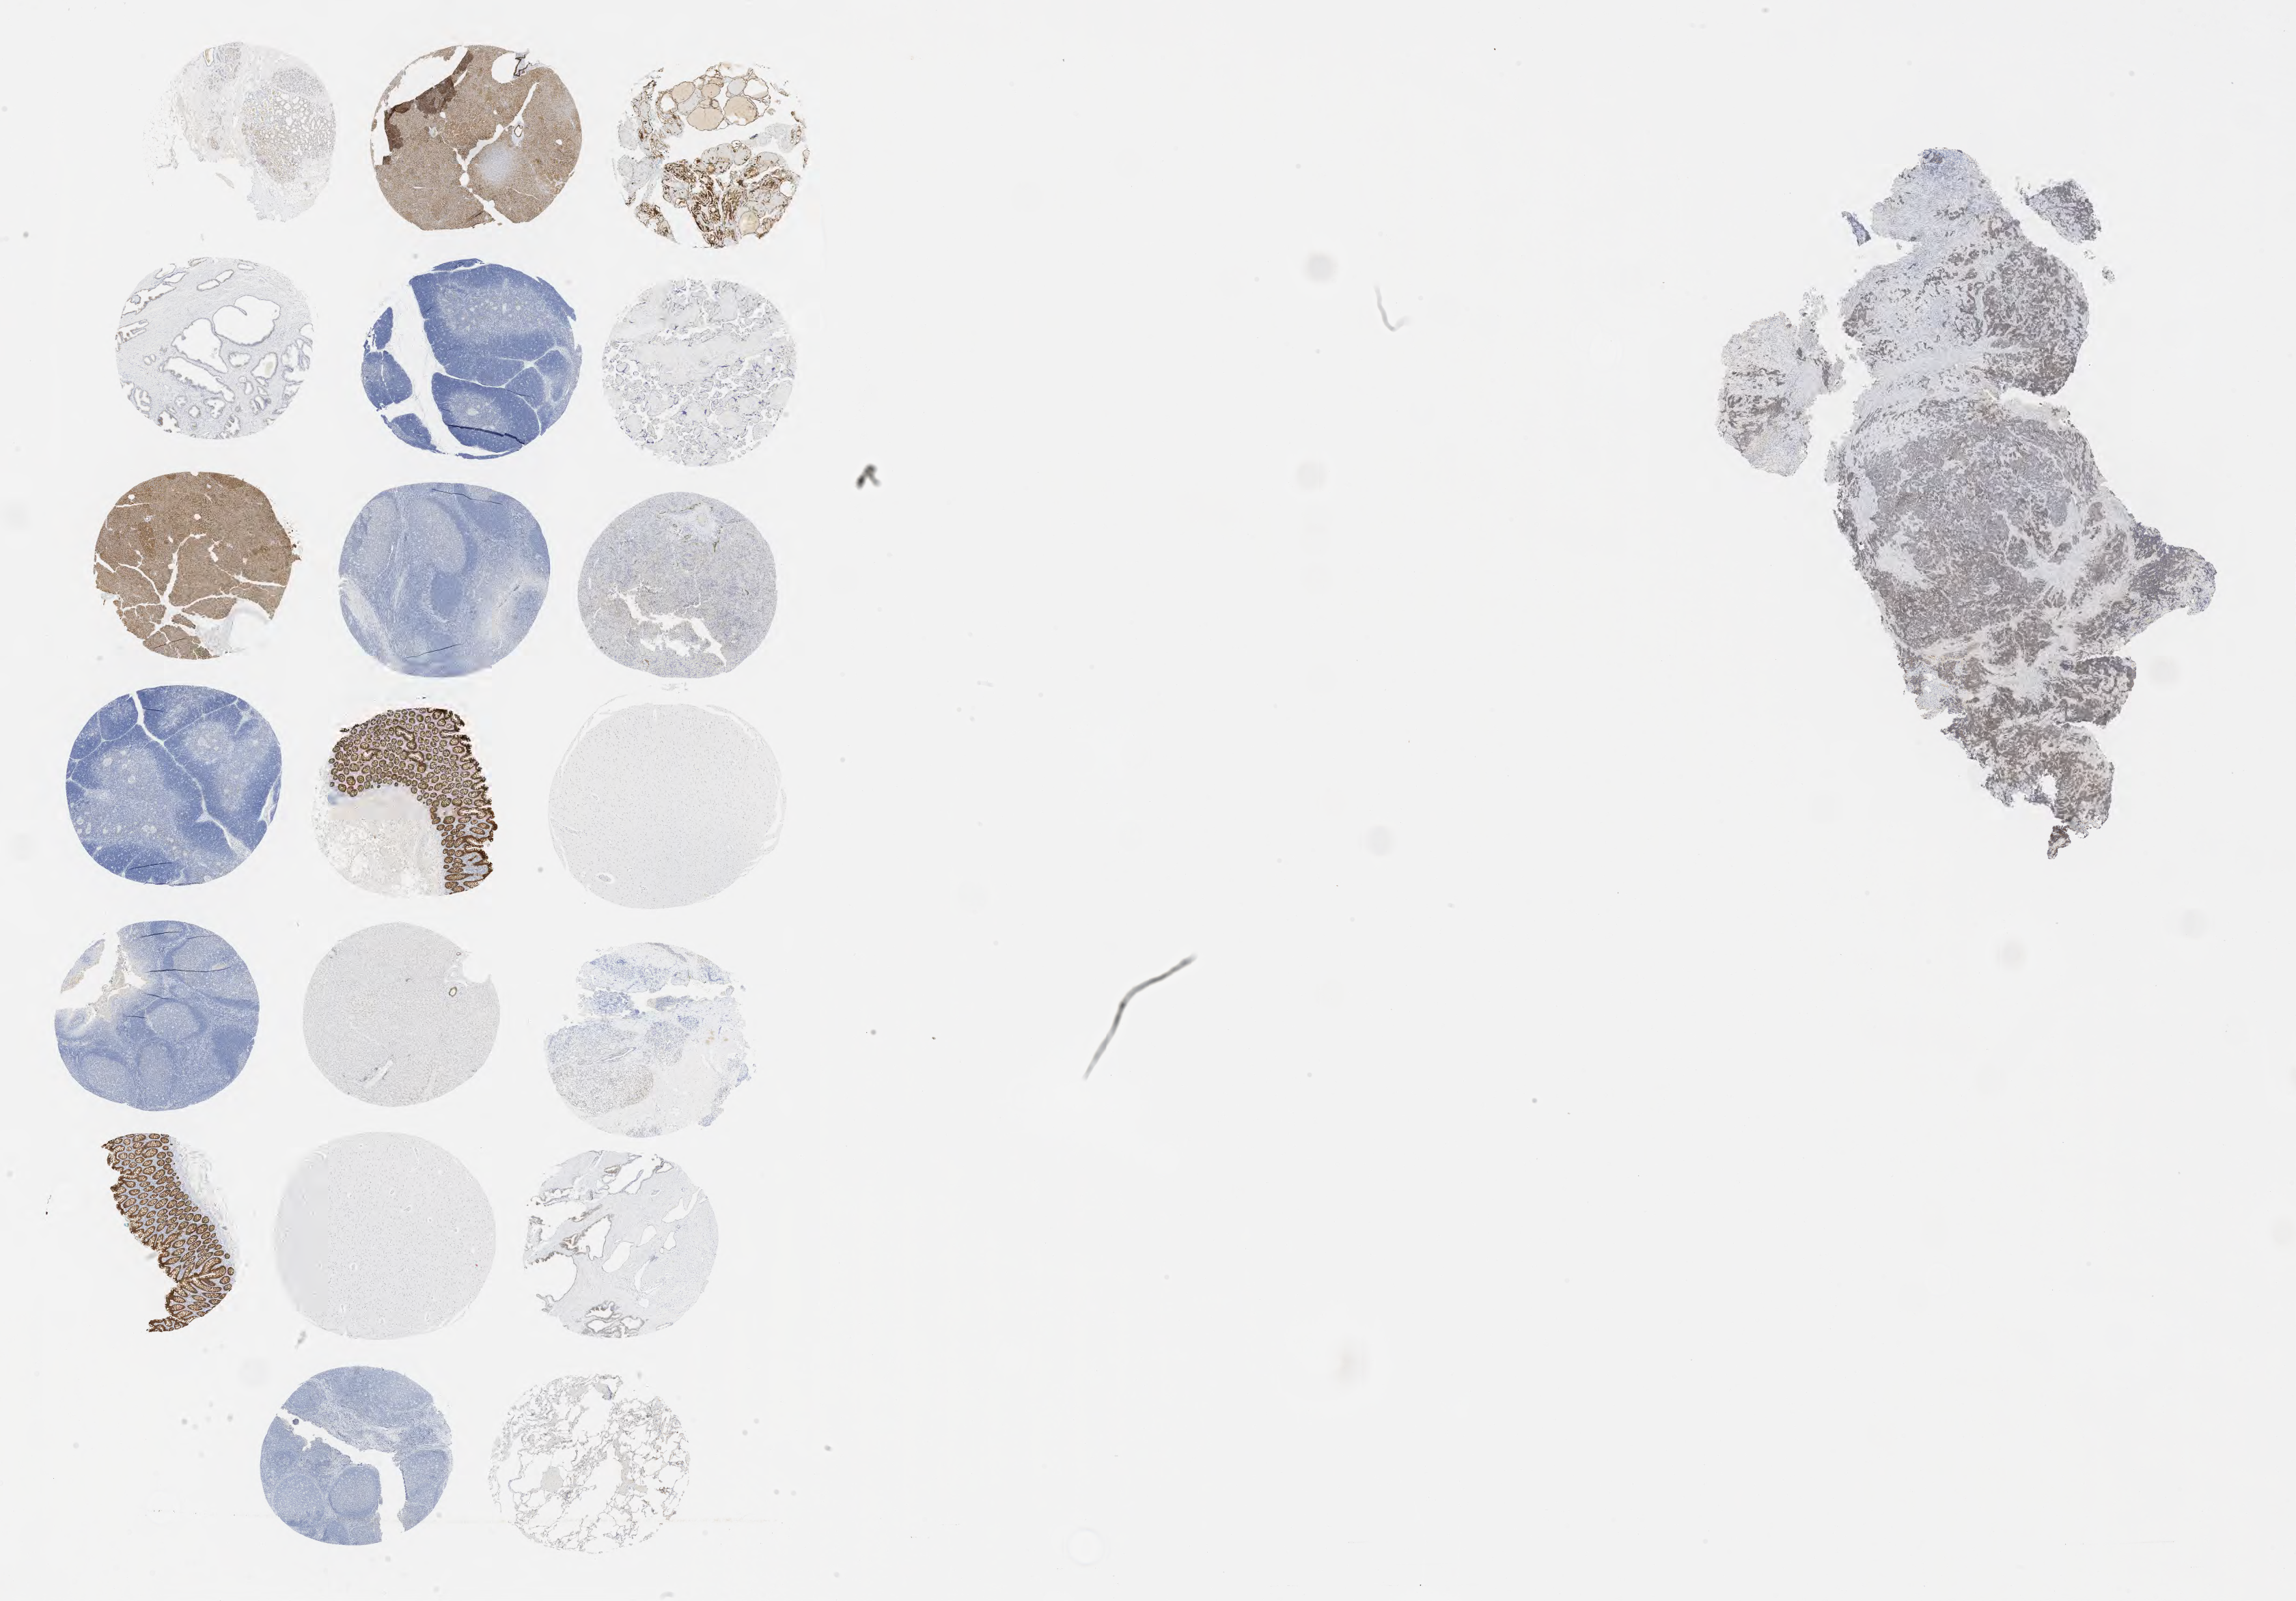
Immunohistochemistry (IHC) whole-slide image stained for Ber-EP4 — shown as a low-resolution overview of the whole scanned area (about 27.2 x 18.9 mm); specimen: tumor tissue; site: cervix. Patient: female, age 43 years.
Histologic diagnosis: Lymphoepithelial carcinoma.